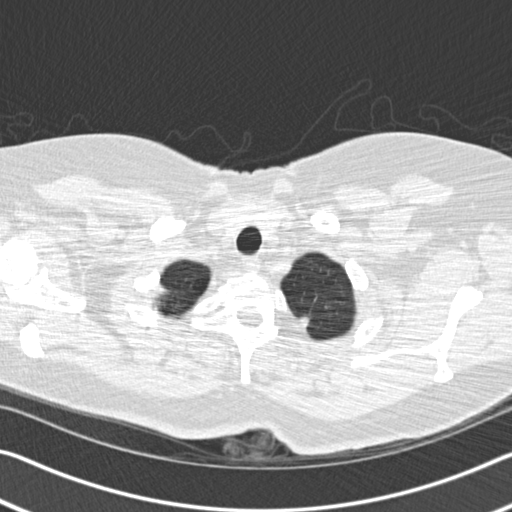
Low-dose screening chest CT, axial slice, first (baseline) screen, lung window (W 1500 / L -600 HU), 120 kVp, 512 × 512 image matrix, field of view 338 × 338 mm. Female participant, aged 60 years at enrolment. Former smoker at enrolment.
• Expert-annotated lung lesion, bounding box (x1, y1, x2, y2) in pixels: (279, 304, 326, 344).
• Screening reader's record for this exam: no non-calcified nodule ≥4 mm recorded.
• Official screen result: negative screen, minor abnormalities not suspicious for lung cancer.
• Later outcome: lung cancer diagnosed 799 days after this screen — non-small cell carcinoma, left upper lobe, poorly differentiated (G3), stage IB (AJCC 6th edition), 16 mm at pathology.